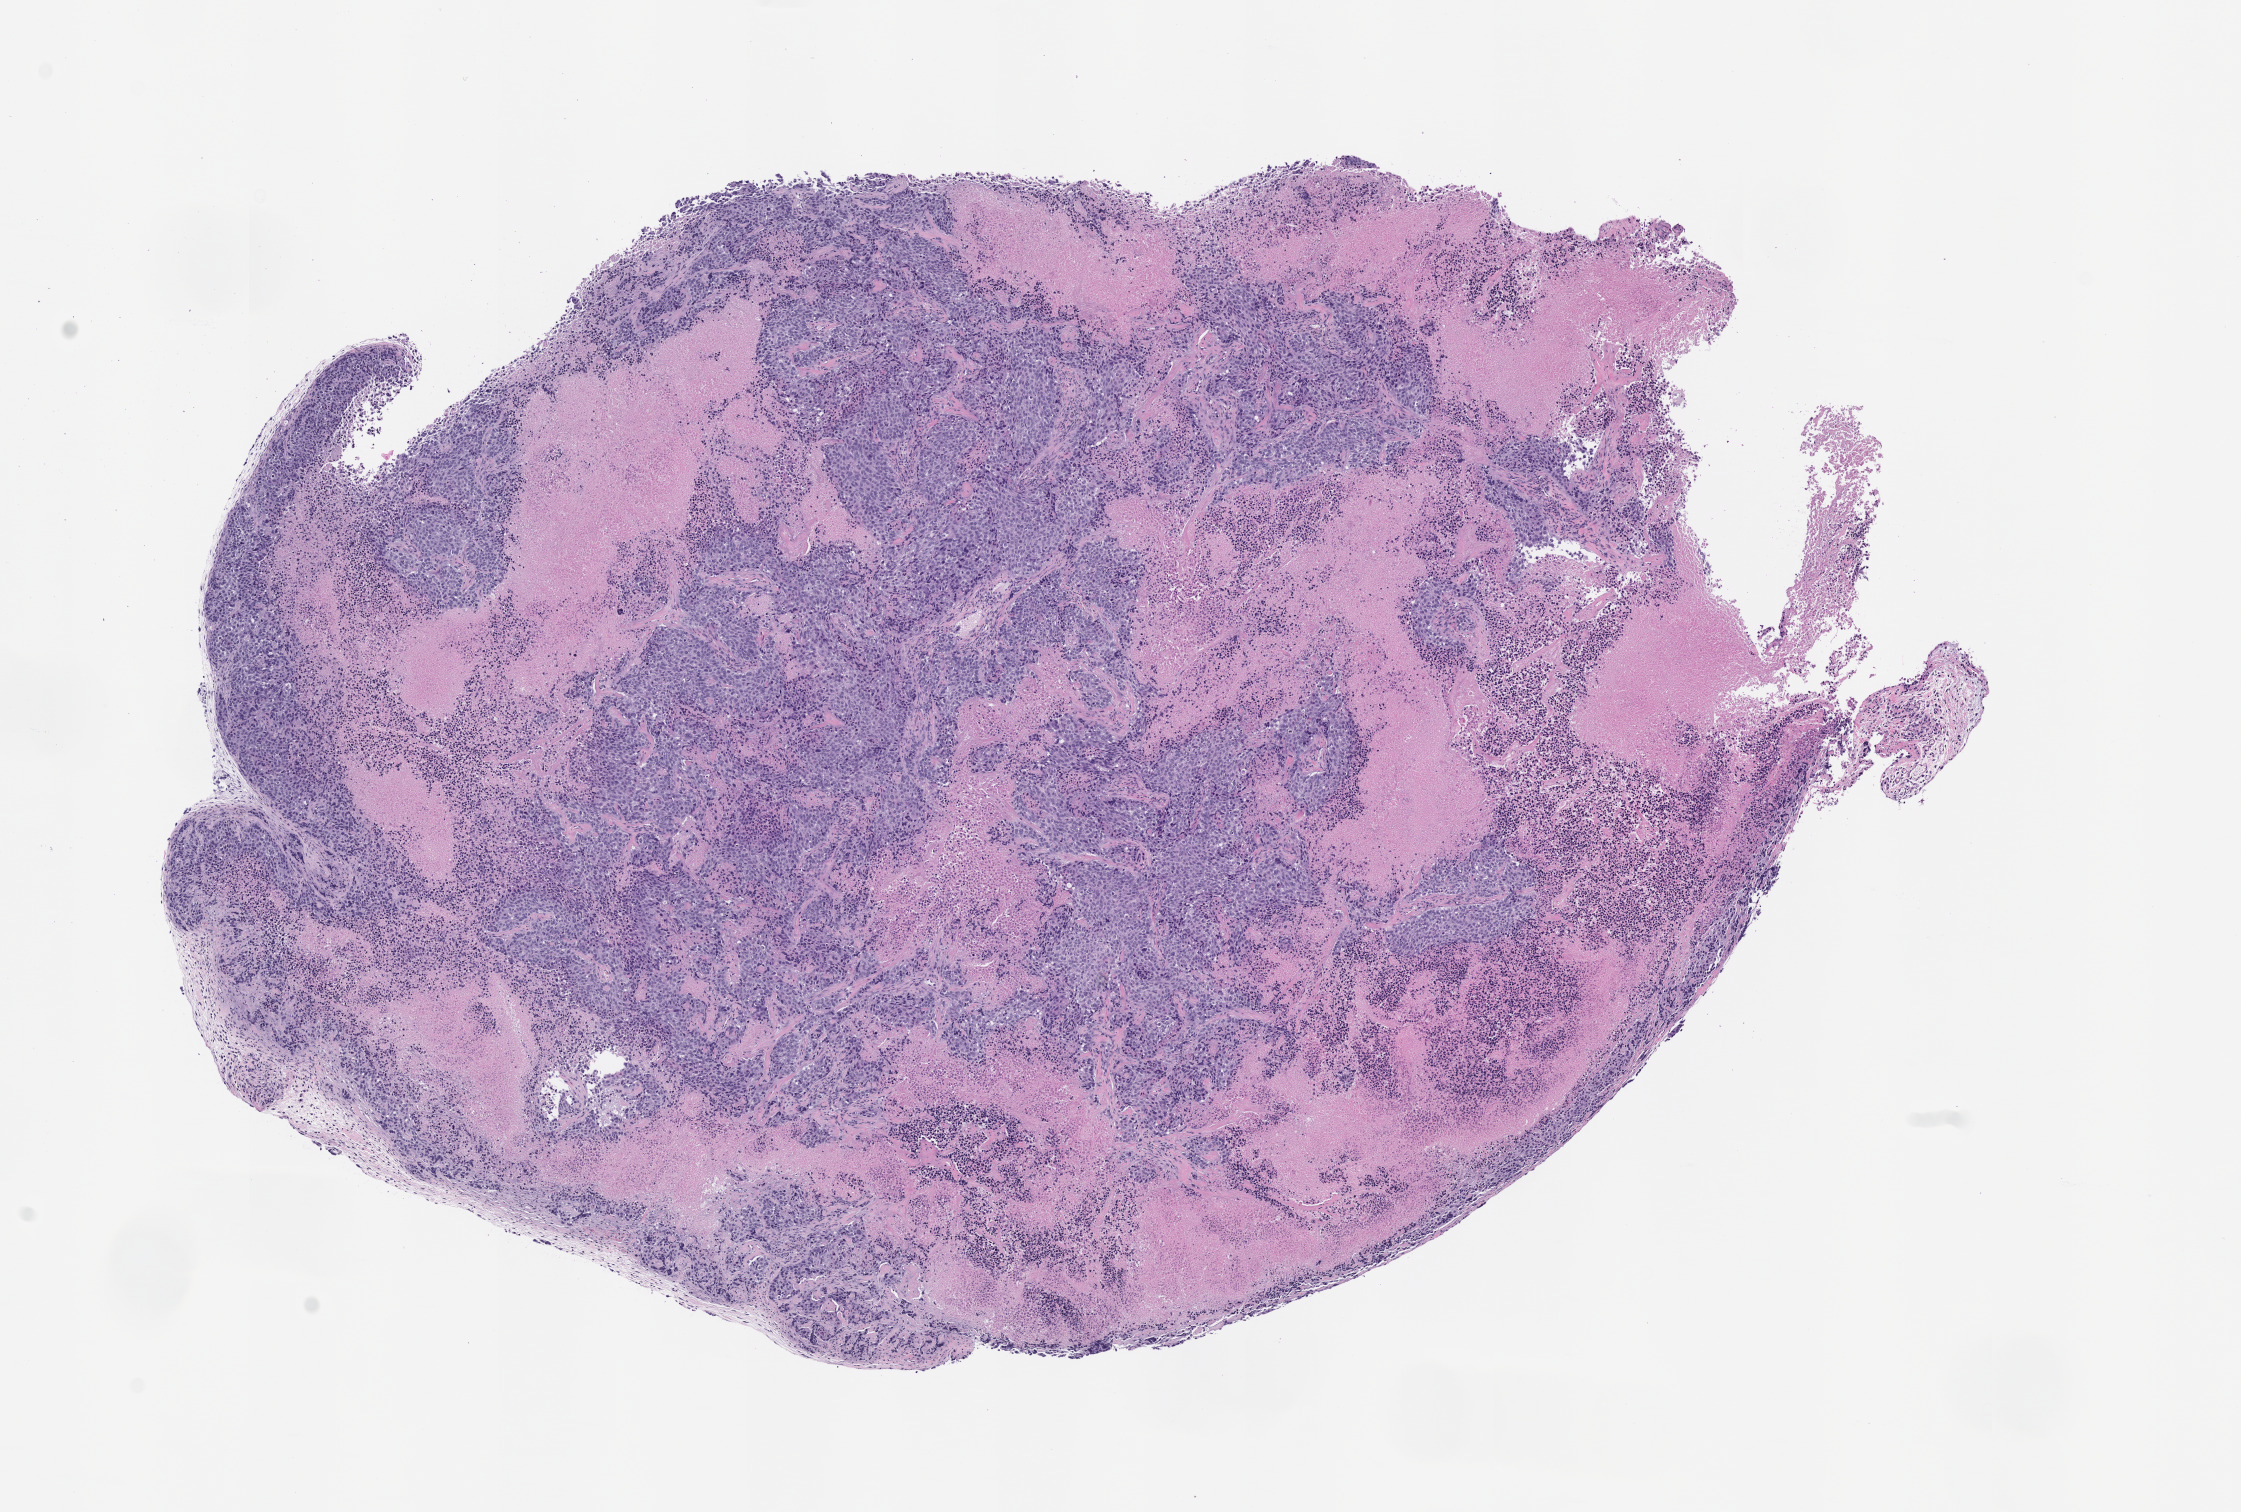
Haematoxylin and eosin whole-slide image of a patient-derived xenograft (PDX) tumor grown in a mouse, passage 1, low-resolution overview of the scanned area, about 9.0 x 6.1 mm; FFPE section; originating tumor site category: lung.
Originating patient diagnosis: Lung Squamous Cell Carcinoma.